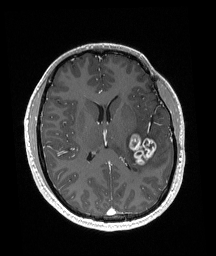
Brain MRI from a brain-tumour surgery series, one axial slice; slice 81 of 192 in the series (ordered by position); T1-weighted post-contrast; 1 mm slice thickness; 216 × 256 image matrix, field of view 211 × 250 mm. From the clinical record (not read from this slice): histopathology: Glioneuronal tumor; WHO grade: 2; tumour location: Left Superior Temporal Gyrus.
Outlined on this slice (expert manual segmentation):
- tumour: bounding box (x1, y1, x2, y2) in pixels: (129, 135, 157, 165)